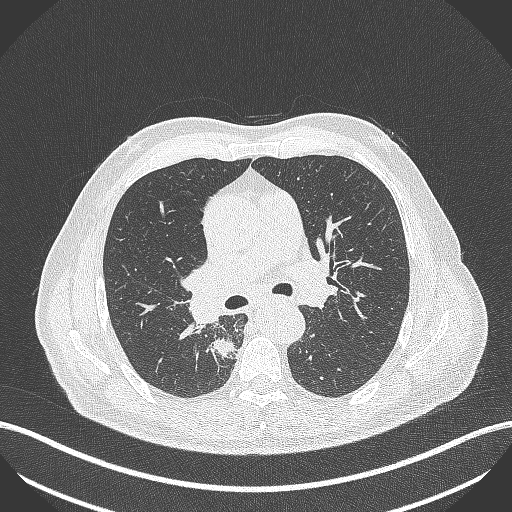
Chest CT, one axial slice; position 282 of 451 along the scan axis; 100 kVp; lung window (W 1500 / L -600 HU); 1 mm slice thickness; 512 × 512 image matrix, field of view 400 × 400 mm. Patient: male, 61 years. Case-level facts recorded for this patient, not image findings: clinical TNM (as recorded): T1 N0 M0.
Annotated regions visible in this slice (rectangle marked by the reading radiologist):
- lung tumour (recorded histology: small cell carcinoma): bounding box (x1, y1, x2, y2) in pixels: (212, 335, 242, 361)